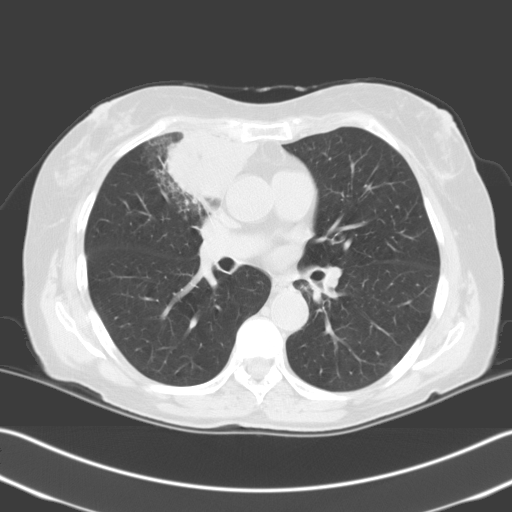
Low-dose screening chest CT, one axial slice. Position 121 of 204 along the scan axis. 140 kVp. Lung window (W 1500 / L -600 HU). 3.2 mm slice thickness. 512 × 512 image matrix, field of view 348 × 348 mm.
Annotated regions visible in this slice (manually delineated by an expert):
- lesion 1 (tumor, upper lobe of right lung): bounding box [x1, y1, x2, y2] px = [164, 131, 257, 208]